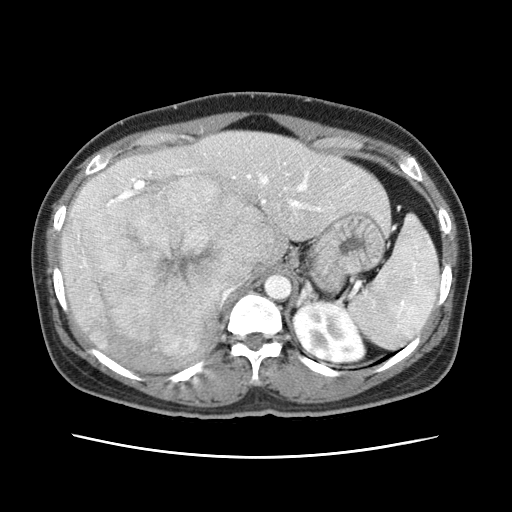
Contrast-enhanced abdominal CT (liver protocol), one axial slice. 120 kVp. Soft-tissue window (W 400 / L 40 HU). 2.5 mm slice thickness. 512 × 512 image matrix, field of view 340 × 340 mm. From the clinical record (not read from this slice): diagnosis: hepatocellular carcinoma (patient treated with transarterial chemoembolisation; whether this scan precedes or follows treatment is not stated here); TNM stage (as recorded): Stage-I; Child-Pugh class: A.
Structures marked on this image (semi-automatically segmented with operator editing):
- abdominal aorta: bounding box (x1, y1, x2, y2) in pixels: (265, 274, 292, 300)
- liver parenchyma outside the tumour (the mass and vessels are separate outlines, so this box may not span the whole liver): (60, 132, 388, 369)
- mass: (77, 175, 285, 354)
- liver vessels: (118, 170, 349, 211)